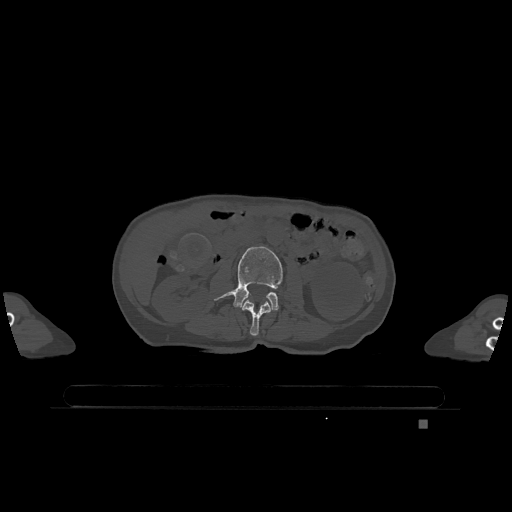
CT including the spine, one axial slice. Slice 379 of 1317 in the series (ordered by position). Bone window (W 1800 / L 400 HU). 0.5 mm slice thickness. 512 × 512 image matrix, field of view 500 × 500 mm. Patient: female, 74 years. From the clinical record (not read from this slice): primary cancer: lung.
Structures marked on this image (semi-automatic segmentation, software-assisted and operator-edited):
- L2 vertebra: bounding box (x1, y1, x2, y2) in pixels: (242, 300, 272, 336)
- L3 vertebra: (214, 246, 283, 310)